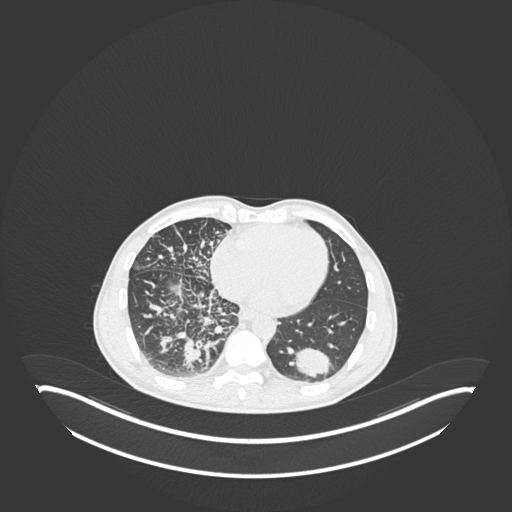
Chest CT, one axial slice; reconstruction kernel B30f; 120 kVp; lung window (W 1500 / L -600 HU); 1 mm slice thickness; 512 × 512 image matrix, field of view 500 × 500 mm. Male patient, age 49 years. Case-level facts recorded for this patient, not image findings: clinical TNM (as recorded): T2b N1 M0.
Annotated regions visible in this slice (rectangle marked by the reading radiologist):
- lung tumour (recorded histology: adenocarcinoma): bounding box <287,345,337,381> (left, top, right, bottom; pixels)